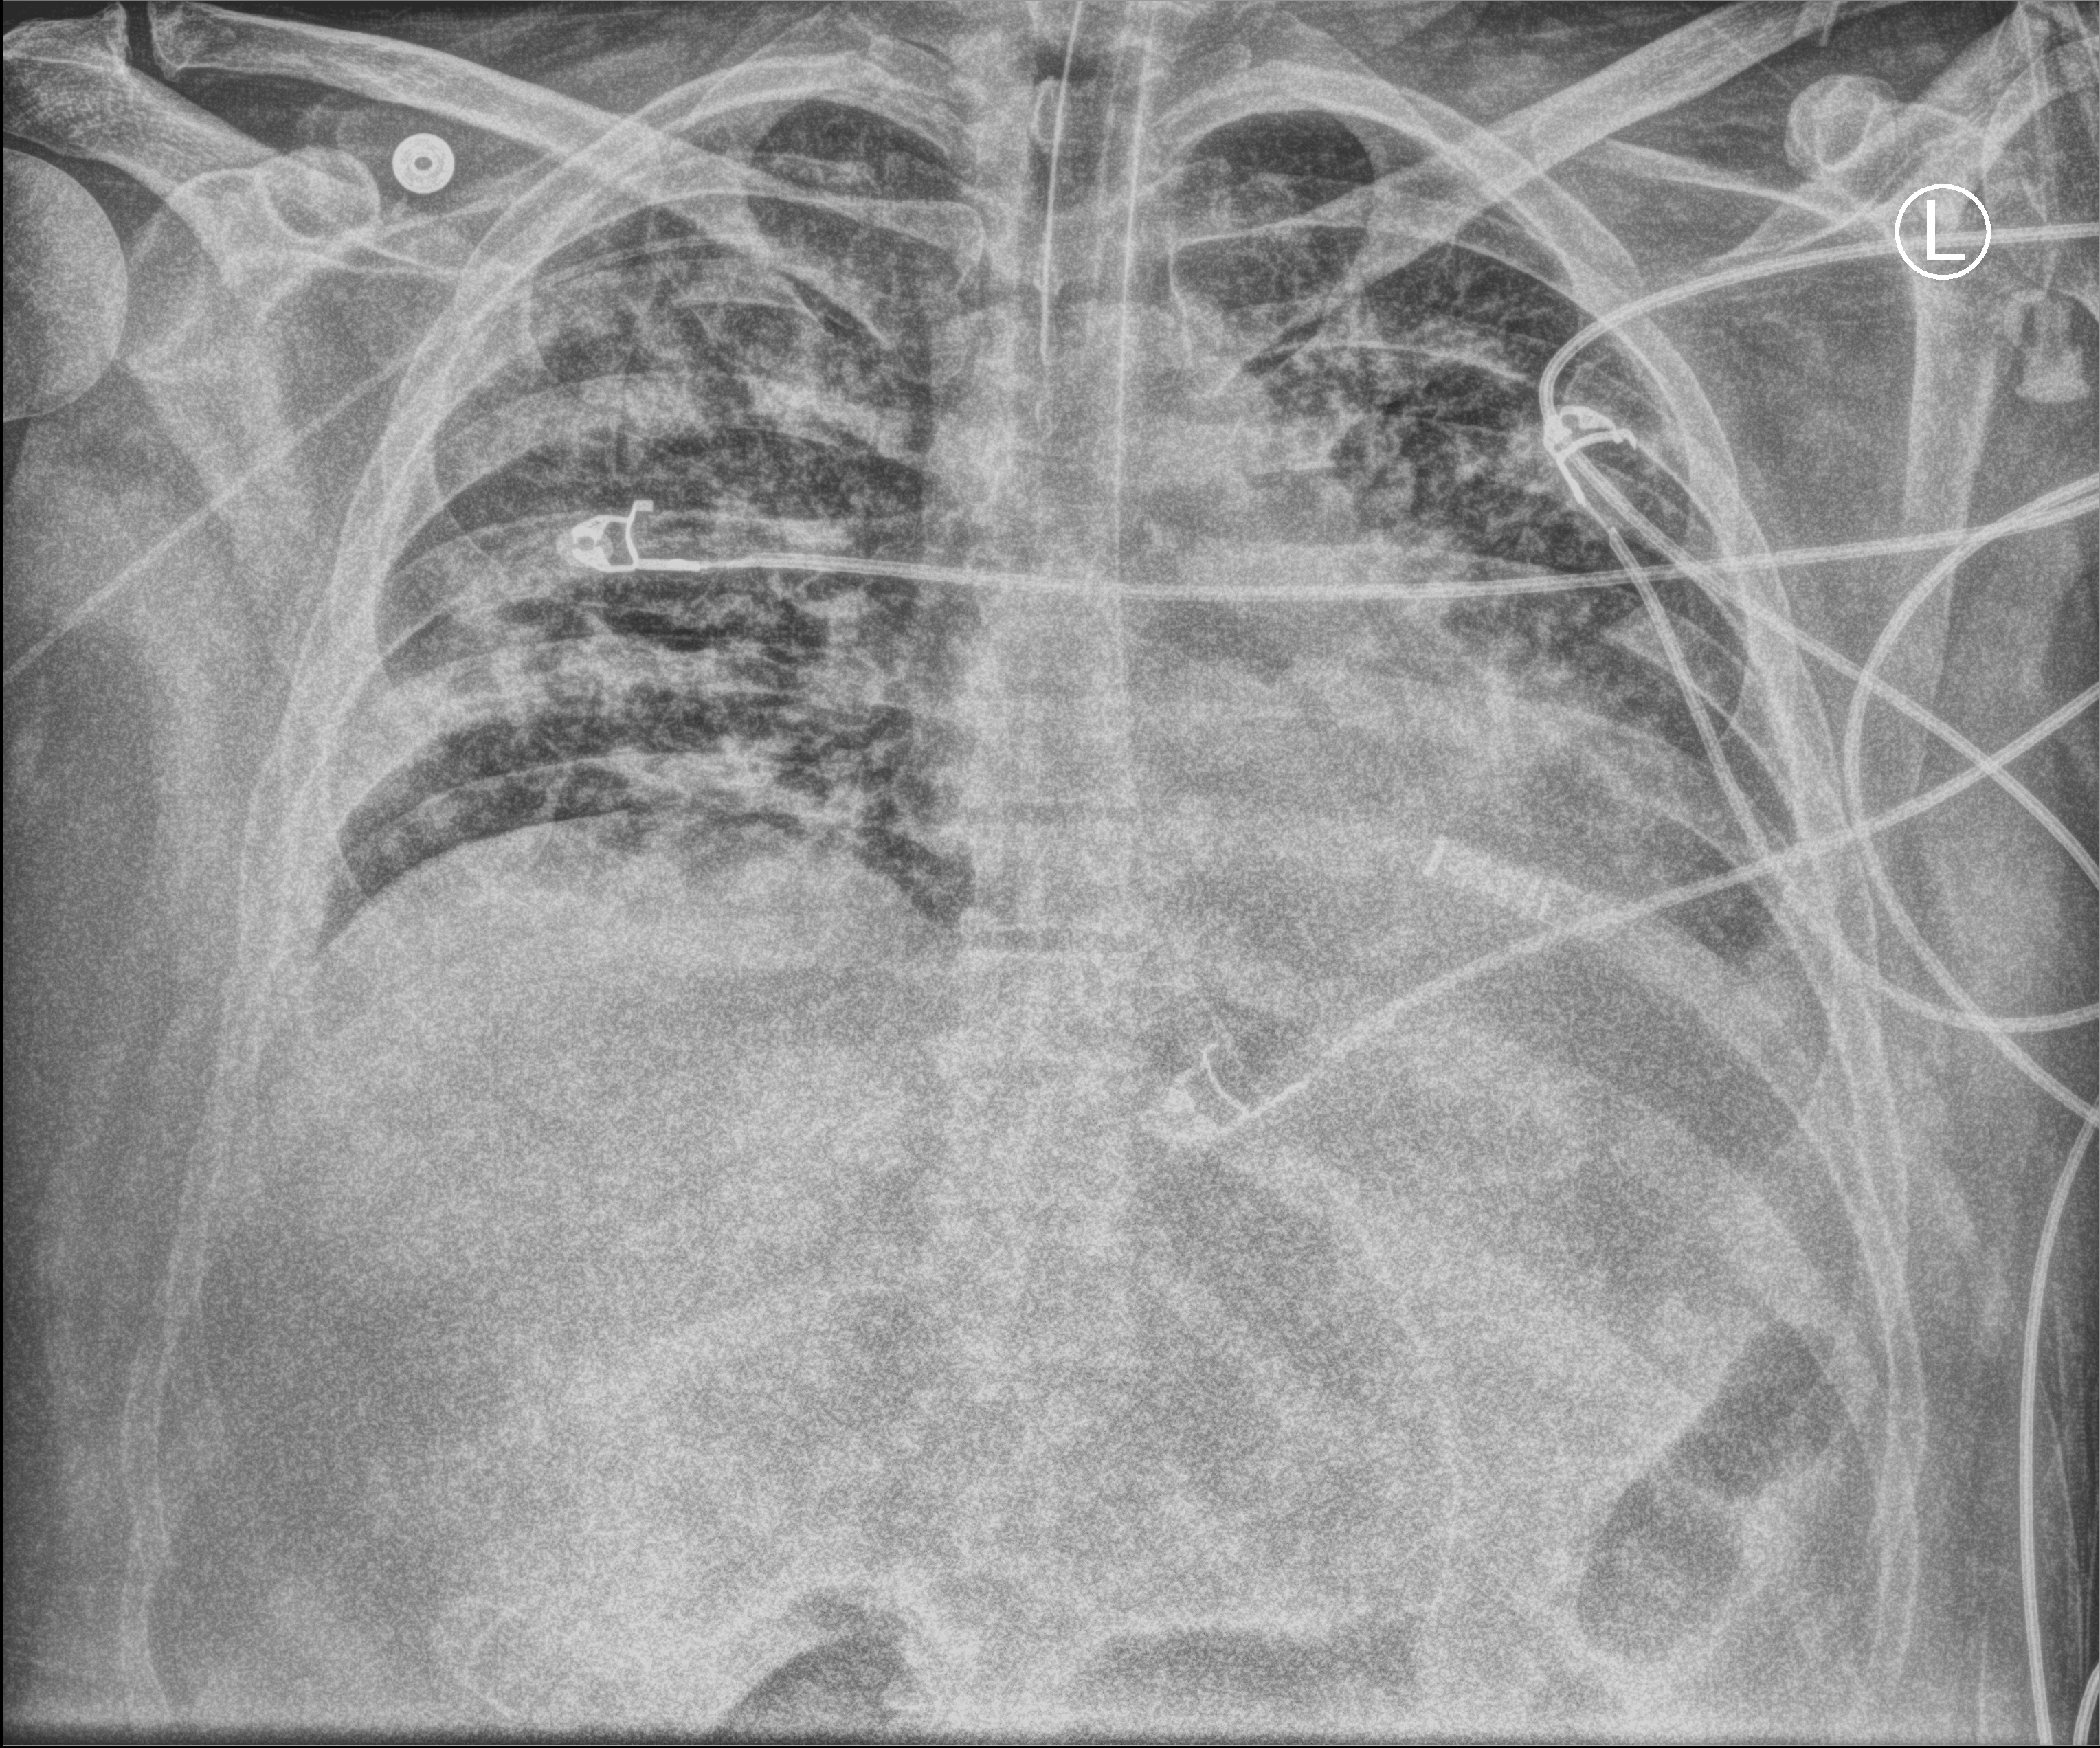
Portable chest radiograph; anteroposterior (AP) projection. Patient hospitalised with COVID-19; male, aged 18–59 years.
Admission-level facts for this patient (not findings on this image; timing relative to this image not recorded): admitted to intensive care during this hospital stay: yes.